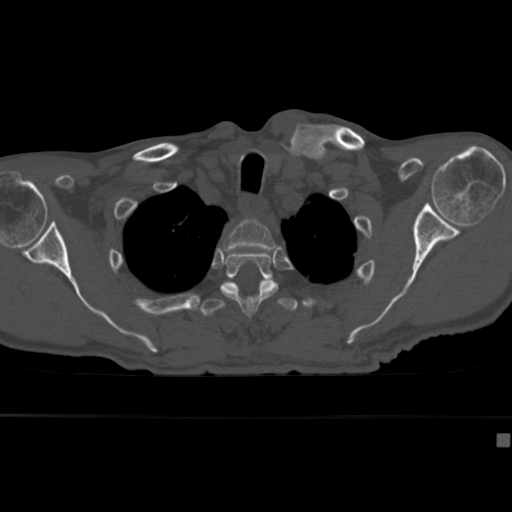
CT including the spine, one axial slice; position 332 of 430 along the scan axis; reconstruction kernel Br40s; 120 kVp; bone window (W 1800 / L 400 HU); 512 × 512 image matrix, field of view 337 × 337 mm. Male patient, age 64 years. From the clinical record (not read from this slice): primary cancer: uterus.
Annotated regions visible in this slice (semi-automatically segmented with operator editing):
- T2 vertebra: bounding box (x1, y1, x2, y2) in pixels: (222, 219, 275, 258)
- T3 vertebra: (220, 252, 279, 316)
- T4 vertebra: (200, 289, 298, 317)